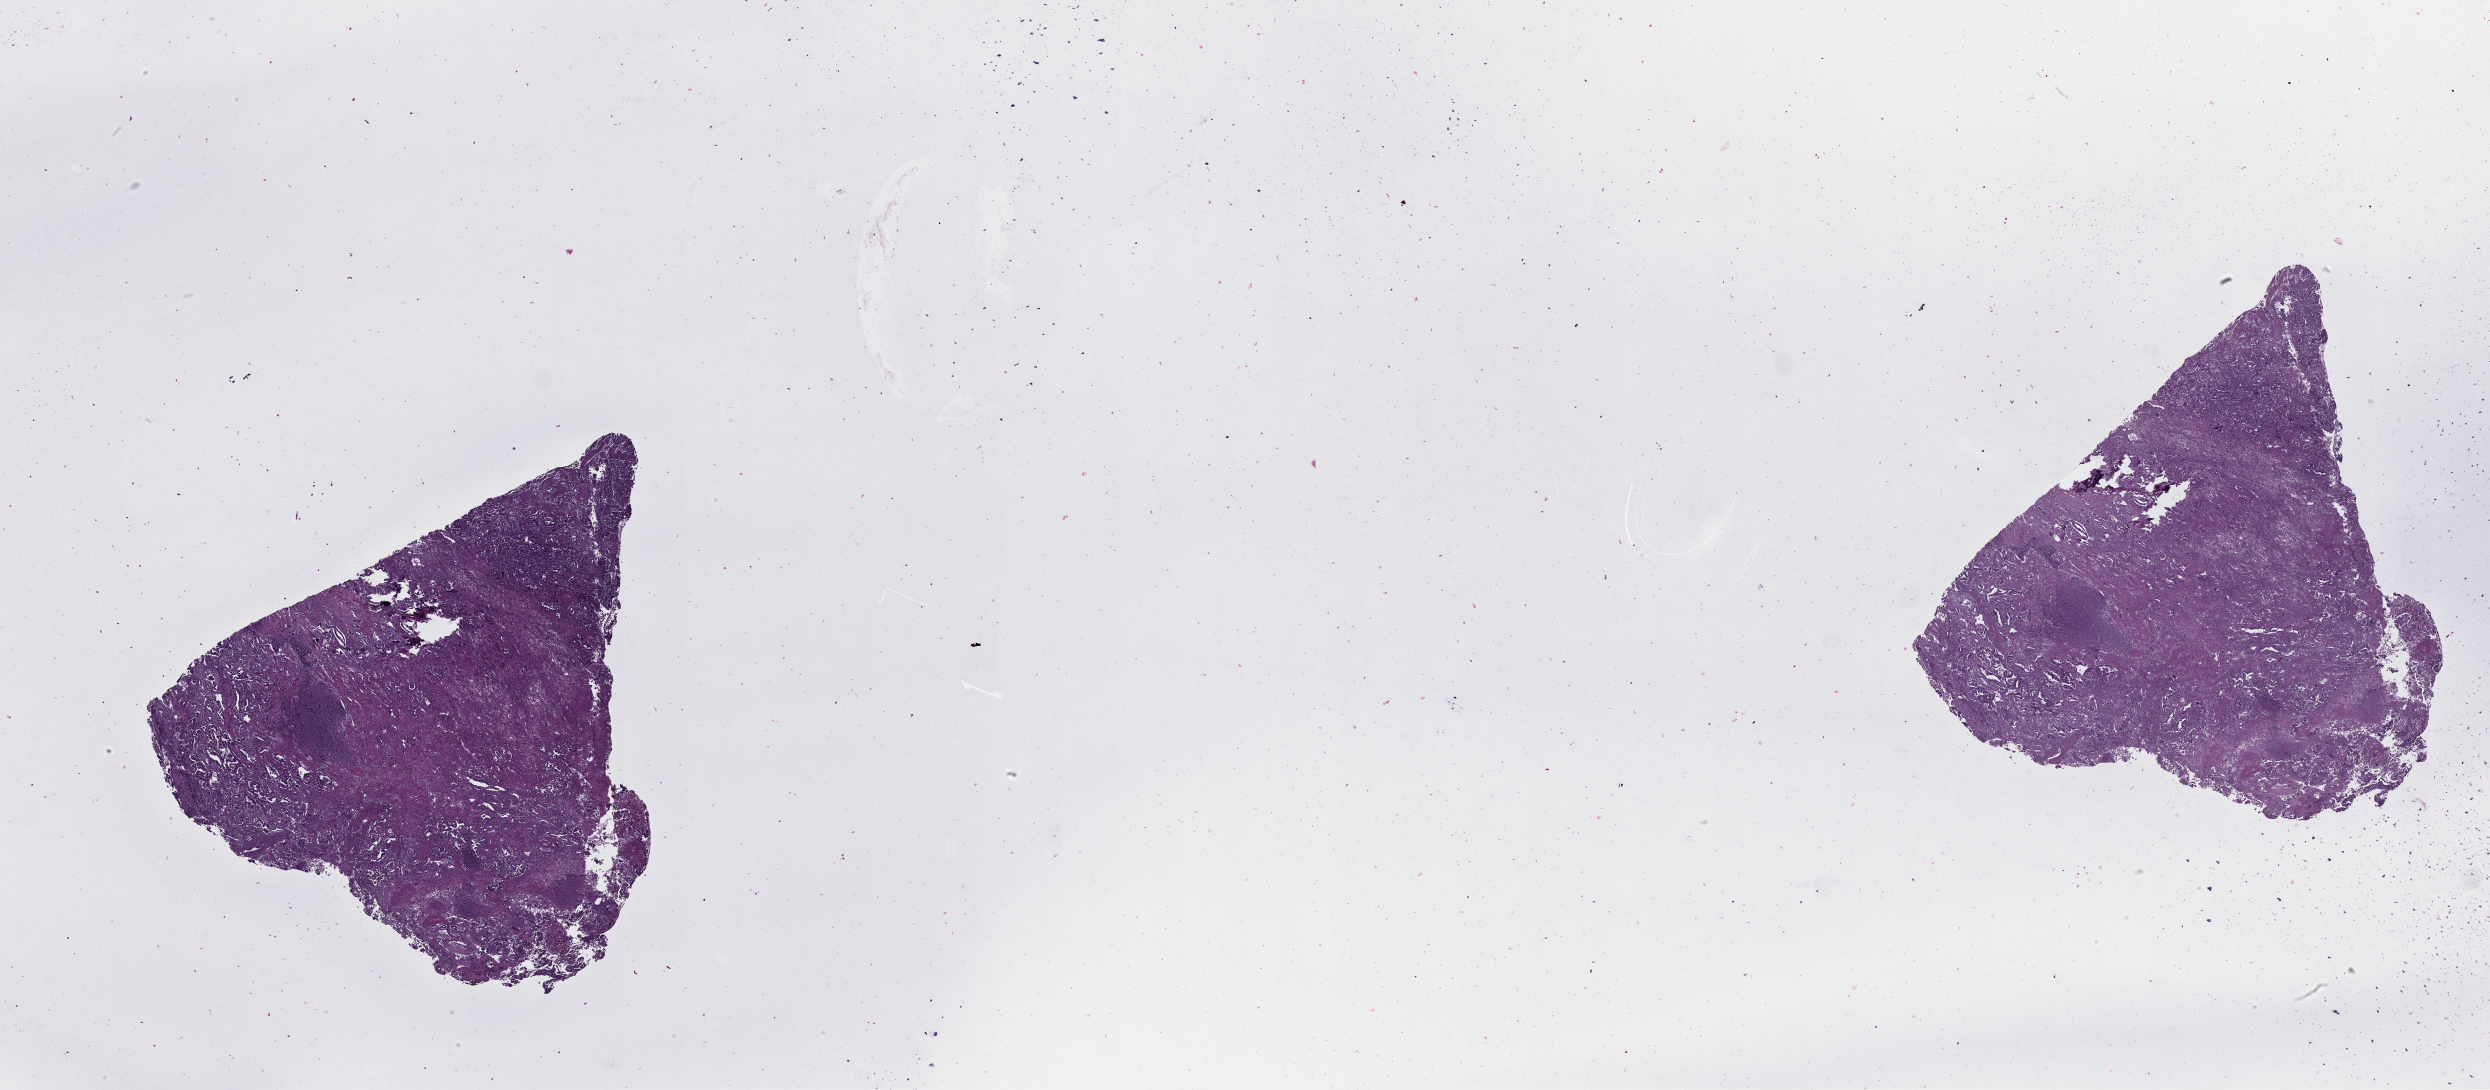
Digitized H&E tissue section (whole slide), low-resolution overview of the scanned area, about 40.1 x 17.5 mm (acquisition: 20x scan). Lung, tissue type not recorded.
Patient diagnosis (cohort enrolment): lung adenocarcinoma (lung).